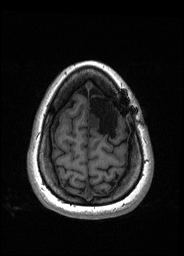
Pre-operative brain MRI before brain-tumour surgery, one axial slice; slice 39 of 176 in the series (ordered by position); T1-weighted post-contrast; 184 × 256 image matrix. From the clinical record (not read from this slice): histopathology: Oligodendroglioma; WHO grade: 2; IDH mutation: yes.
Annotated regions visible in this slice (expert manual segmentation):
- tumour: bounding box [x1, y1, x2, y2] px = [88, 112, 100, 128]